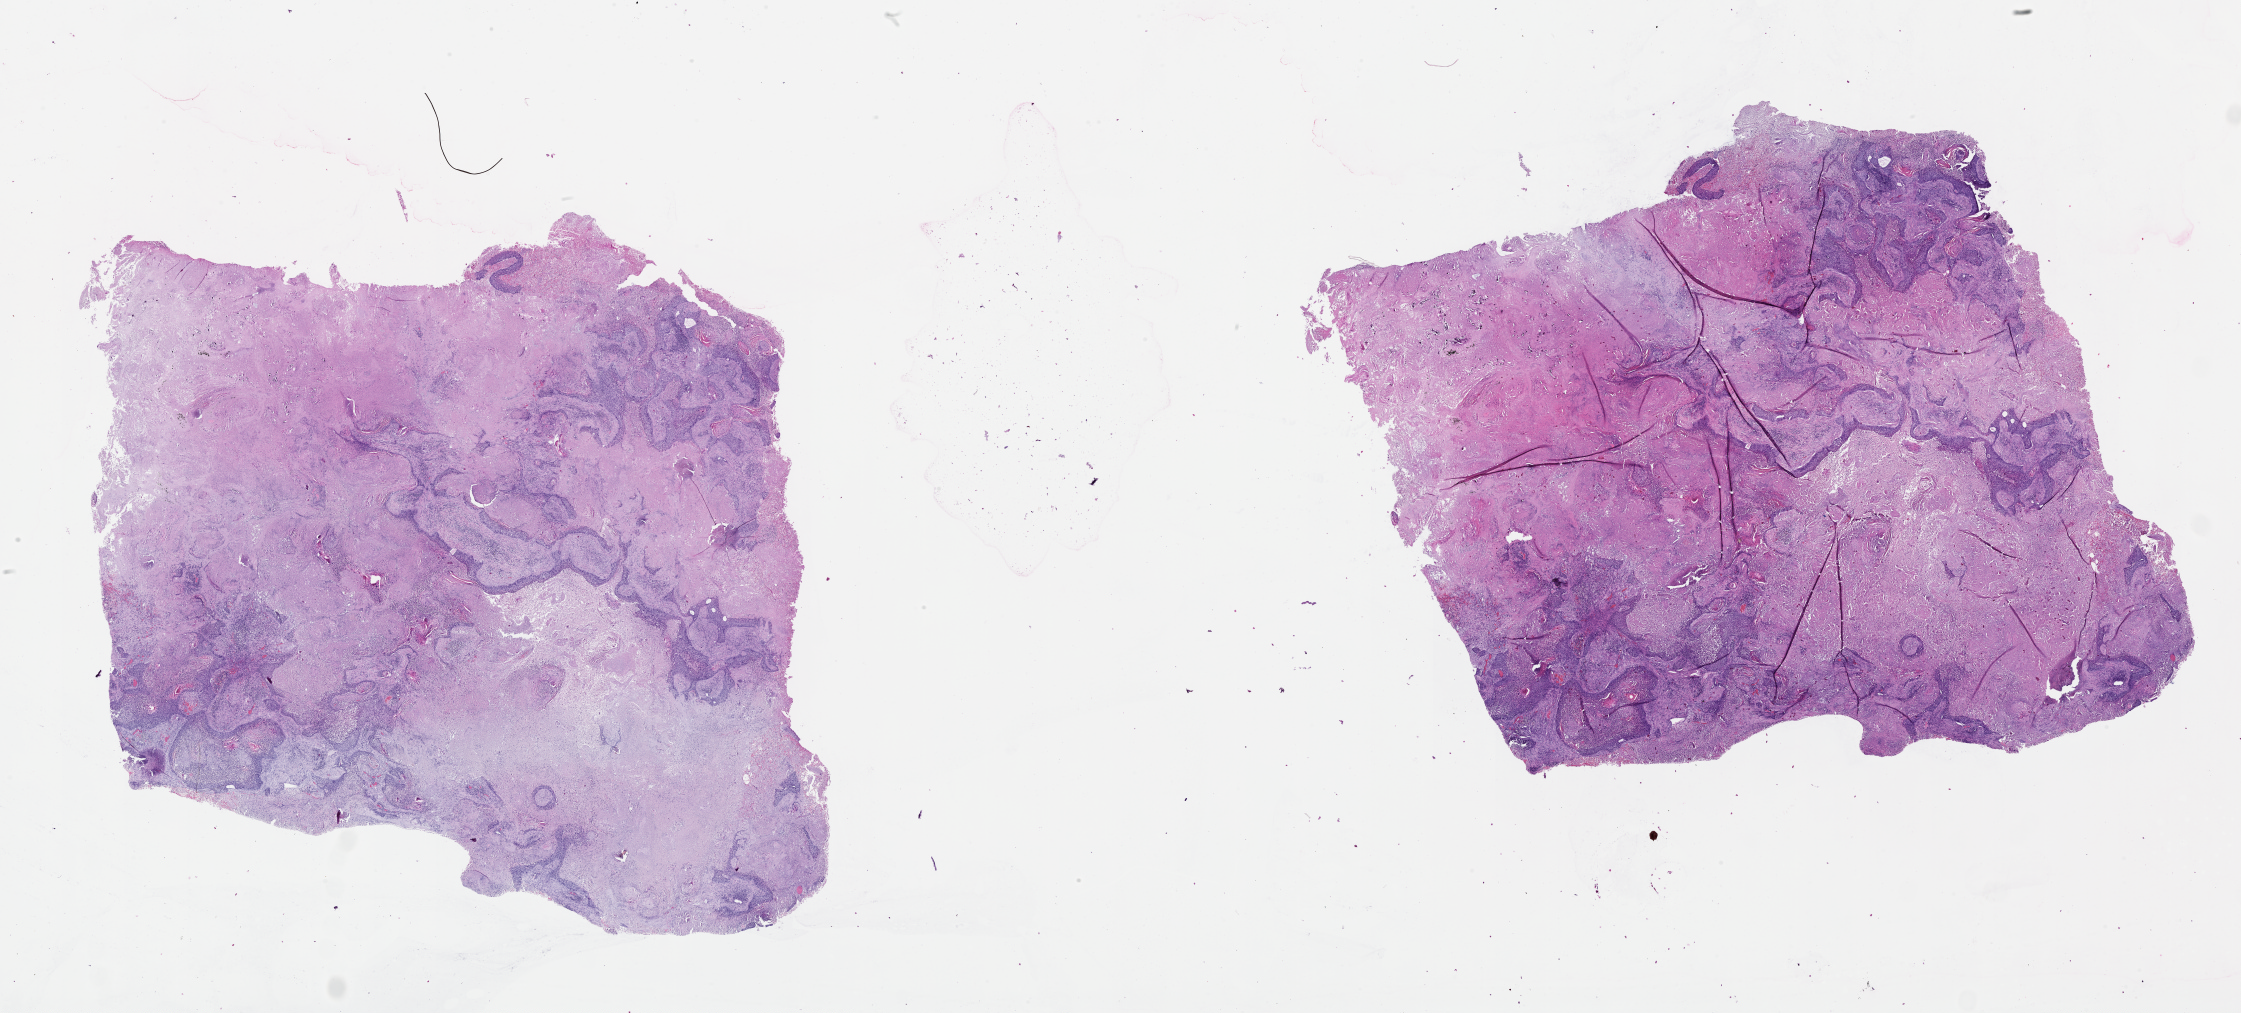
H&E whole-slide image — a low-resolution overview of the entire scanned area, about 36.1 x 16.3 mm, tumour tissue sample, lung. 49-year-old male patient.
* patient diagnosis (cohort enrolment): squamous cell carcinoma (lung)